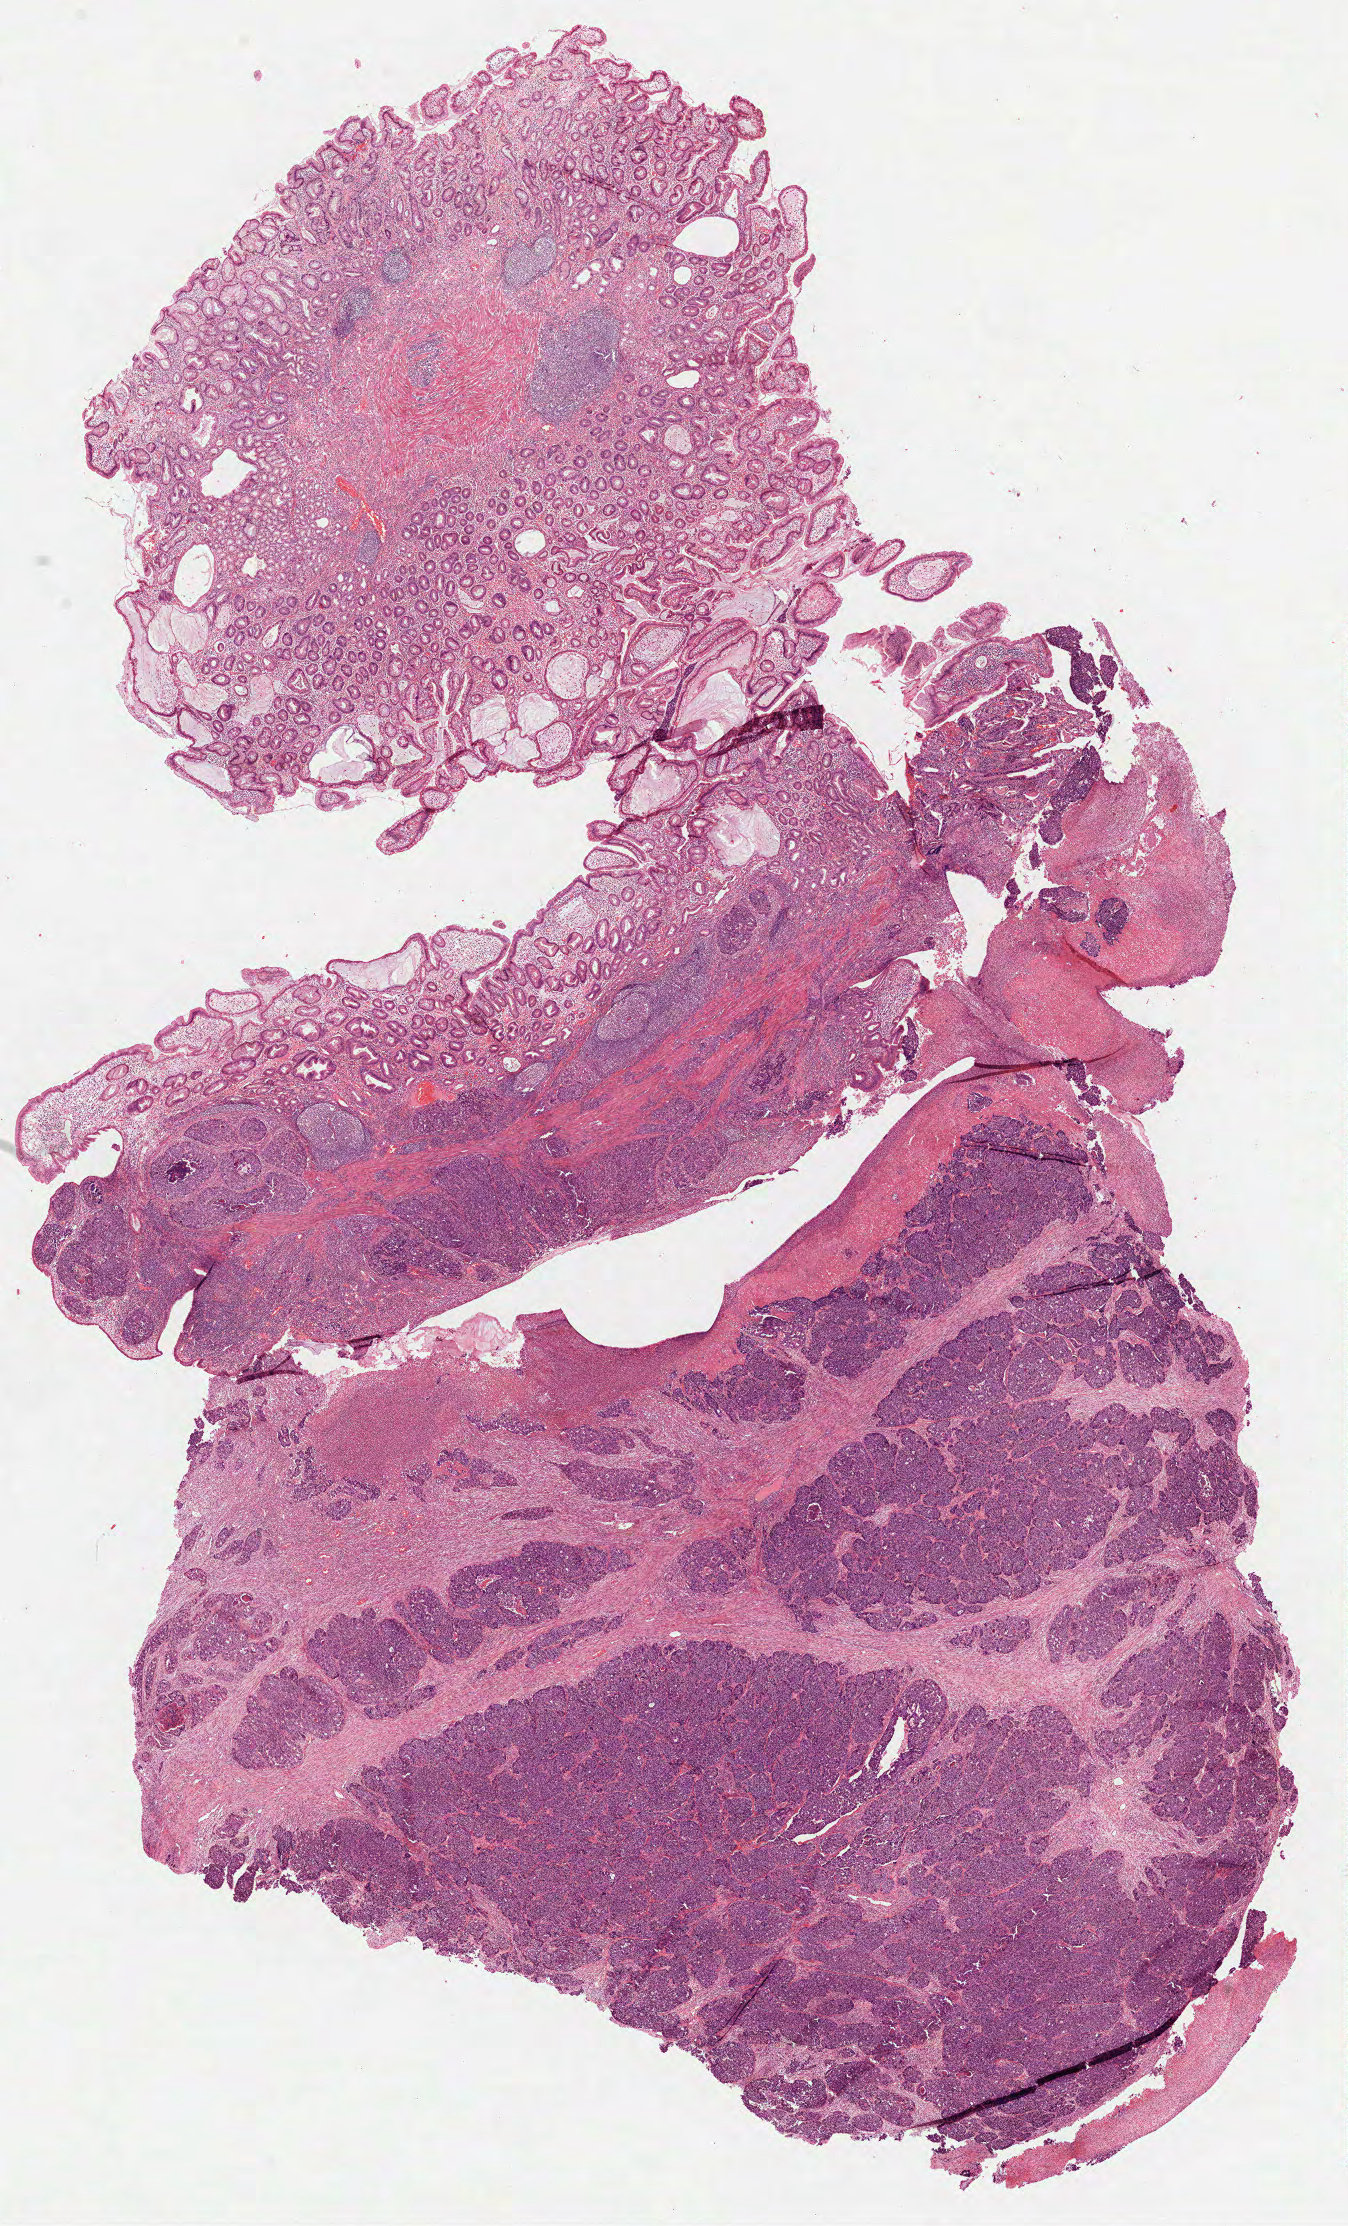
Digitized H&E tissue section (whole slide), a low-resolution overview of the entire scanned area, about 10.9 x 18.0 mm (acquisition: 40x scan); formalin-fixed paraffin-embedded (FFPE) diagnostic section; stomach, primary tumour sample. Male patient; age at initial diagnosis 76 years. Histologic grade: G2 (moderately differentiated).
- AJCC pathologic stage: IB
- histologic diagnosis: Adenocarcinoma, NOS